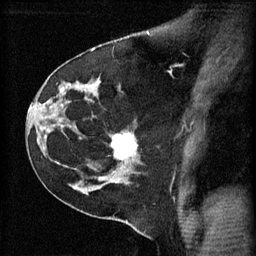
Breast MRI (dynamic contrast-enhanced), one sagittal slice. Position 39 of 60 along the scan axis. 3 images stored at this slice position (order not interpretable as contrast timing). 1.5 T. TE 4.2 ms, TR 11 ms. 2 mm slice thickness. 256 × 256 image matrix. Female patient, age 45 years.
Structures marked on this image (semi-automatically segmented with operator editing):
- analysis volume of interest (the breast-tissue region the enhancement analysis was run in; not a lesion): bounding box (x1, y1, x2, y2) in pixels: (112, 132, 141, 171)
- tumour enhancement mask (voxels above the 70 % enhancement threshold inside the analysis volume of interest): (112, 134, 139, 161)